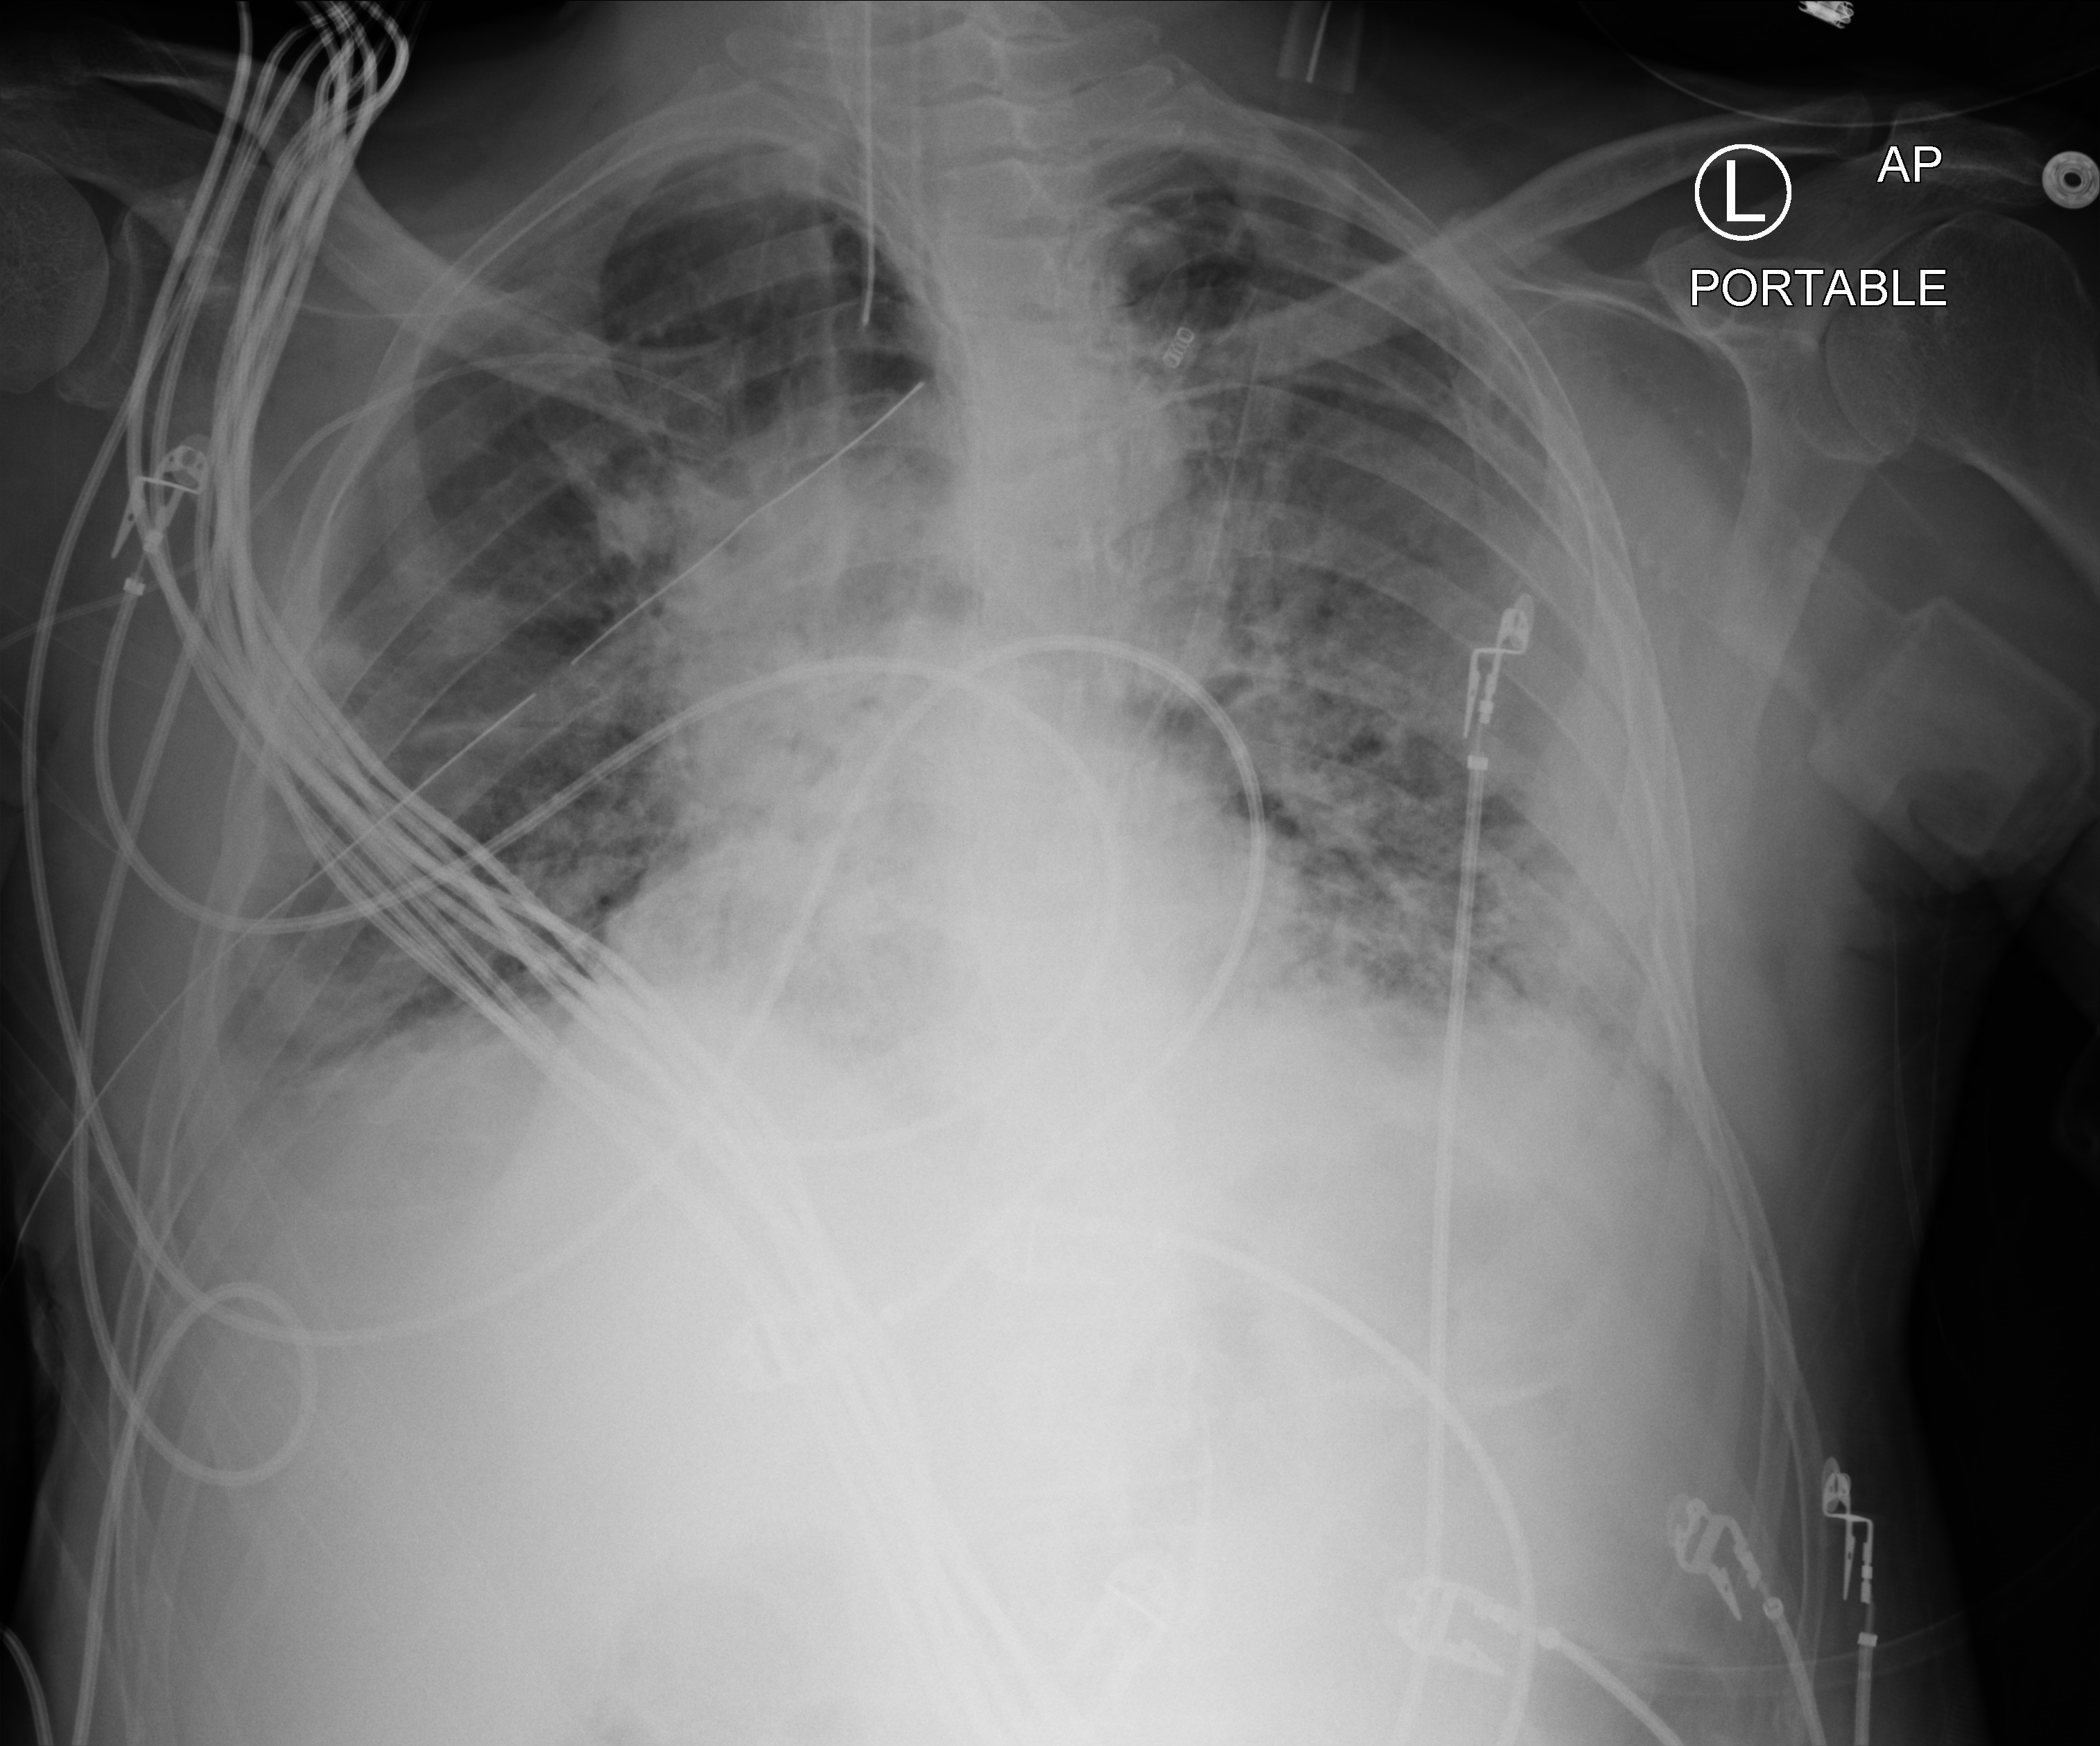
Chest X-ray (portable); anteroposterior (AP) projection. Male patient hospitalised with COVID-19, age 18–59 years.
Hospital-stay facts (about this admission, not read from this image; timing relative to this image not recorded):
- smoking status (admission record): never
- mechanically ventilated during this hospital stay: yes